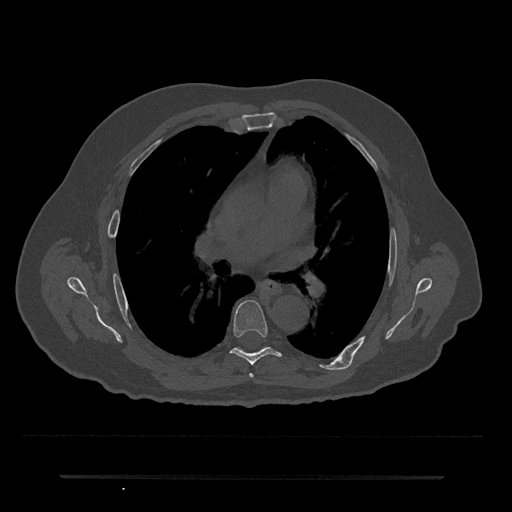
CT including the spine, one axial slice; position 432 of 797 along the scan axis; bone window (W 1800 / L 400 HU); 0.5 mm slice thickness; 512 × 512 image matrix. Patient: male, 69 years. From the clinical record (not read from this slice): primary cancer: prostate.
Structures marked on this image (semi-automatically segmented with operator editing):
- T5 vertebra: bounding box <249,373,253,378> (left, top, right, bottom; pixels)
- T6 vertebra: <230,300,281,365>